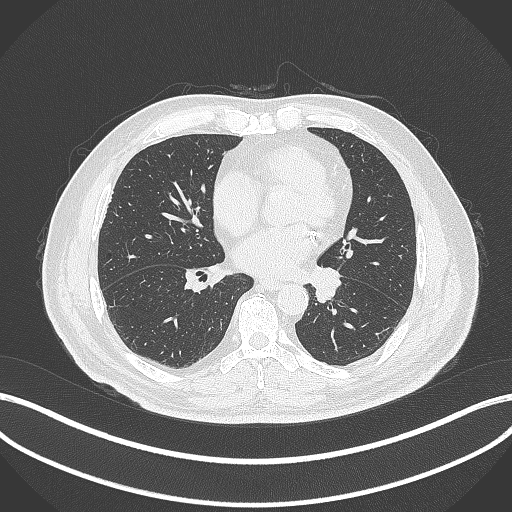
Chest CT, one axial slice; position 124 of 312 along the scan axis; reconstruction kernel B70f; lung window (W 1500 / L -600 HU); 1 mm slice thickness; 512 × 512 image matrix, field of view 400 × 400 mm. Male patient, age 71 years. Case-level facts recorded for this patient, not image findings: clinical TNM (as recorded): T1b N0 M0.
Annotated regions visible in this slice (rectangle marked by the reading radiologist):
- lung tumour (recorded histology: squamous cell carcinoma): bounding box <308,264,345,303> (left, top, right, bottom; pixels)